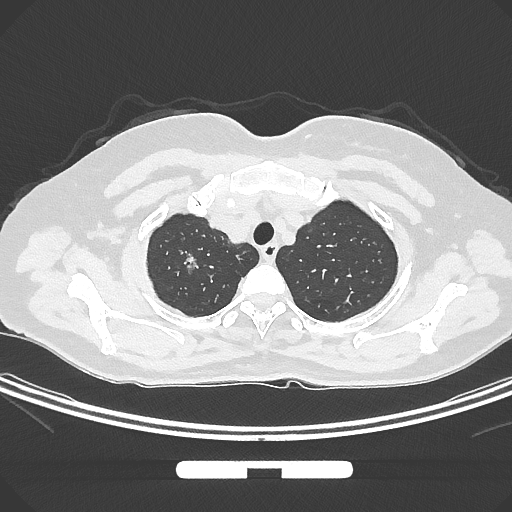
Chest CT, one axial slice. Reconstruction kernel IMR1,SharpPlus. Lung window (W 1500 / L -600 HU). 512 × 512 image matrix, field of view 369 × 369 mm. Female patient, age 58 years. From the clinical record (not read from this slice): clinical TNM (as recorded): T1b N0 M0; histopathological grade: G2-3.
Structures marked on this image (rectangle marked by the reading radiologist):
- lung tumour (recorded histology: adenocarcinoma): bounding box <174,245,204,283> (left, top, right, bottom; pixels)